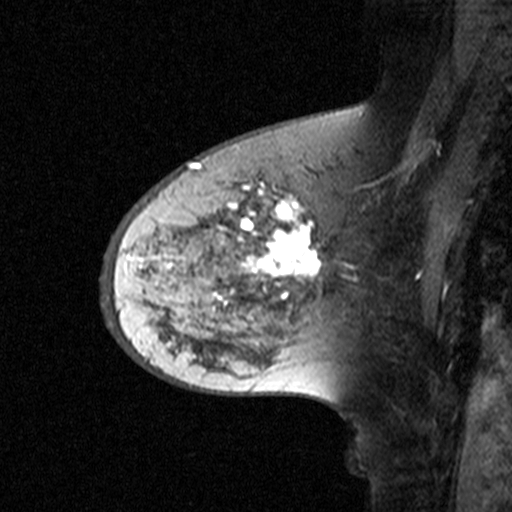
Breast MRI (dynamic contrast-enhanced), one sagittal slice; dynamic contrast-enhanced study with each time point stored as its own series, time point 2 of 3 at this slice position (early post-contrast, ordered by acquisition time); 1.5 T; TE 4.5 ms, TR 11 ms; 3 mm slice thickness; 512 × 512 image matrix, field of view 200 × 200 mm. Patient: female, 65 years. Case-level facts recorded for this patient, not image findings: setting: breast cancer imaged before/during neoadjuvant chemotherapy; receptor status: HER2-positive.
Annotated regions visible in this slice (semi-automatically segmented with operator editing):
- analysis volume of interest (the breast-tissue region the enhancement analysis was run in; not a lesion): box from (x=160, y=172) to (x=329, y=345) px
- tumour enhancement mask (voxels above the 90 % enhancement threshold inside the analysis volume of interest): (x=196, y=178)–(x=320, y=309)